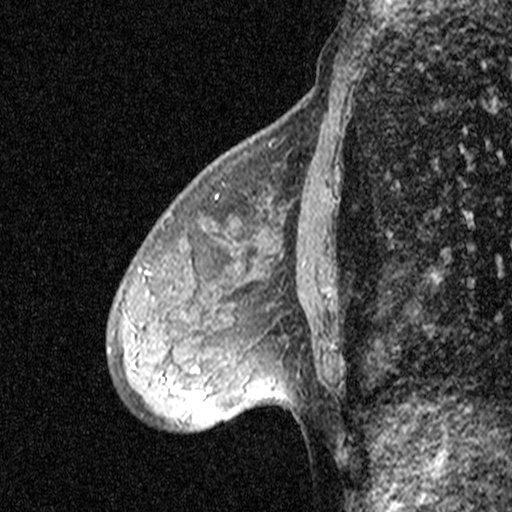
Breast MRI (dynamic contrast-enhanced), one sagittal slice. Slice 16 of 44 in the series (ordered by position). Dynamic contrast-enhanced study with each time point stored as its own series, time point 2 of 3 at this slice position (early post-contrast, ordered by acquisition time). 1.5 T. TE 4.5 ms, TR 11 ms. 3 mm slice thickness. 512 × 512 image matrix, field of view 200 × 200 mm. Female patient, age 53 years. From the clinical record (not read from this slice): setting: breast cancer imaged before/during neoadjuvant chemotherapy; receptor status: HR-positive, HER2-negative.
Annotated regions visible in this slice (semi-automatic segmentation, software-assisted and operator-edited):
- analysis volume of interest (the breast-tissue region the enhancement analysis was run in; not a lesion): box from (x=88, y=176) to (x=313, y=423) px
- tumour enhancement mask (voxels above the 90 % enhancement threshold inside the analysis volume of interest): (x=173, y=389)–(x=185, y=394)